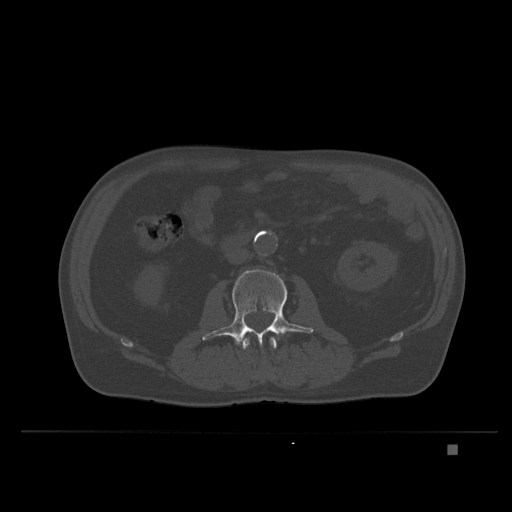
CT including the spine, one axial slice. Position 100 of 435 along the scan axis. Bone window (W 1800 / L 400 HU). 1.5 mm slice thickness. 512 × 512 image matrix. Patient: male, 73 years. Case-level facts recorded for this patient, not image findings: primary cancer: skin.
Annotated regions visible in this slice (semi-automatic segmentation, software-assisted and operator-edited):
- L2 vertebra: bounding box [x1, y1, x2, y2] px = [243, 336, 277, 378]
- L3 vertebra: [202, 269, 314, 347]